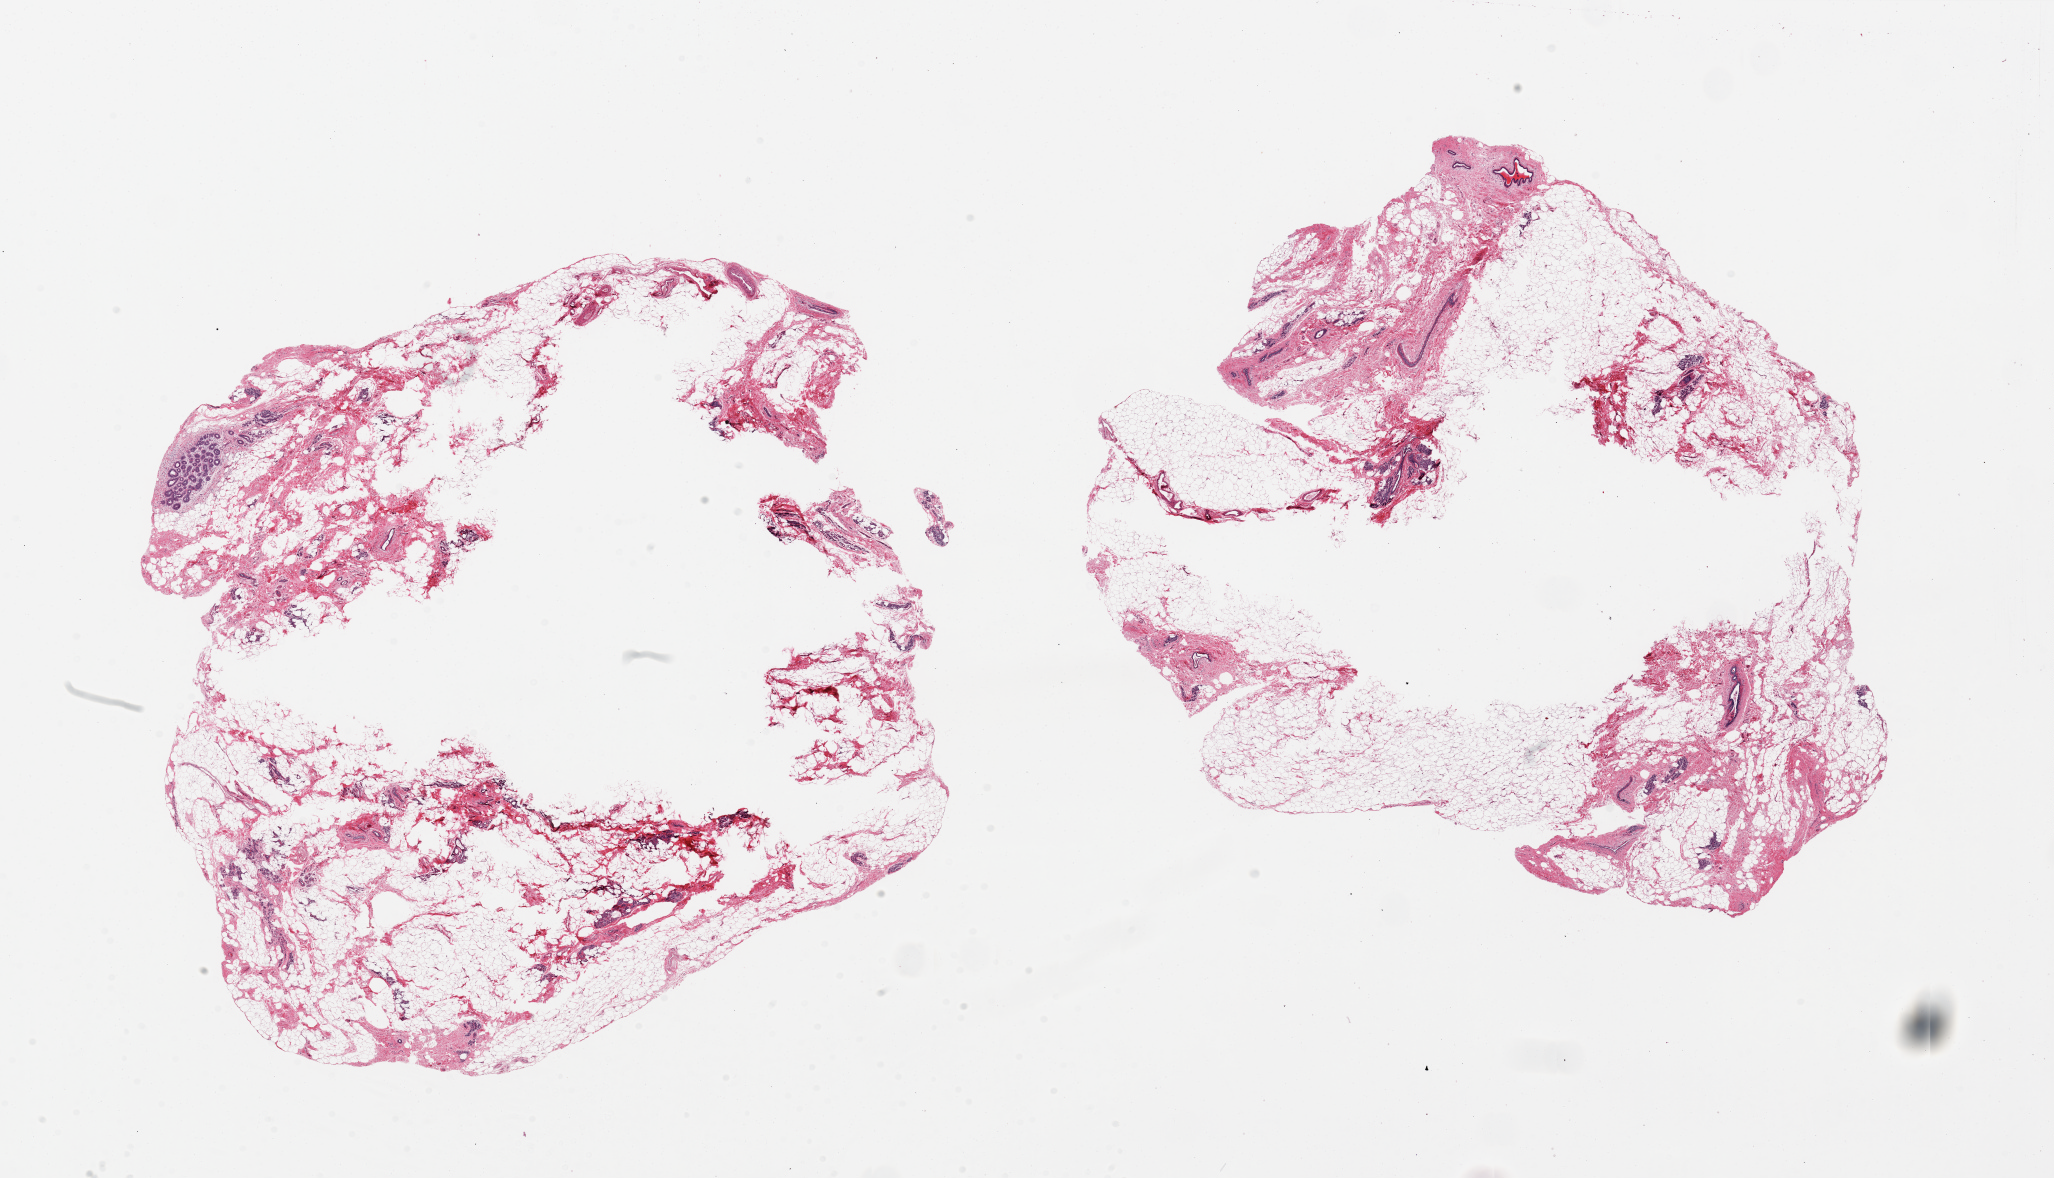
Haematoxylin and eosin whole-slide image, brightfield, whole scanned area (about 32.5 x 18.6 mm) shown as a low-resolution overview. PAXgene-fixed paraffin-embedded (PFPE) section. Section of breast (target tissue). Donor tissue sample. Donor: female.
Pathologist's review note for this sample: 2 pieces, 13x12 & 13x11mm. Scattered small collections of ducts and lobules. Large central (adipose?) empty, unfixed.